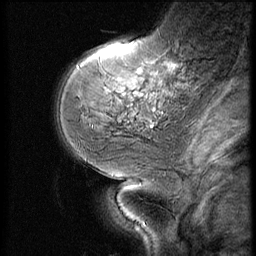
Breast MRI (dynamic contrast-enhanced), one sagittal slice; dynamic contrast-enhanced series, image 2 of 3 at this slice position (ordered by acquisition); 1.5 T; TE 4.2 ms, TR 9 ms; 2.5 mm slice thickness; 256 × 256 image matrix, field of view 180 × 180 mm. Patient: female, 51 years. Case-level facts recorded for this patient, not image findings: setting: breast cancer imaged before/during neoadjuvant chemotherapy; receptor status: triple-negative.
Outlined on this slice (semi-automatically segmented with operator editing):
- analysis volume of interest (the breast-tissue region the enhancement analysis was run in; not a lesion): bounding box <73,46,172,147> (left, top, right, bottom; pixels)
- tumour enhancement mask (voxels above the 140 % enhancement threshold inside the analysis volume of interest): <140,68,142,71>